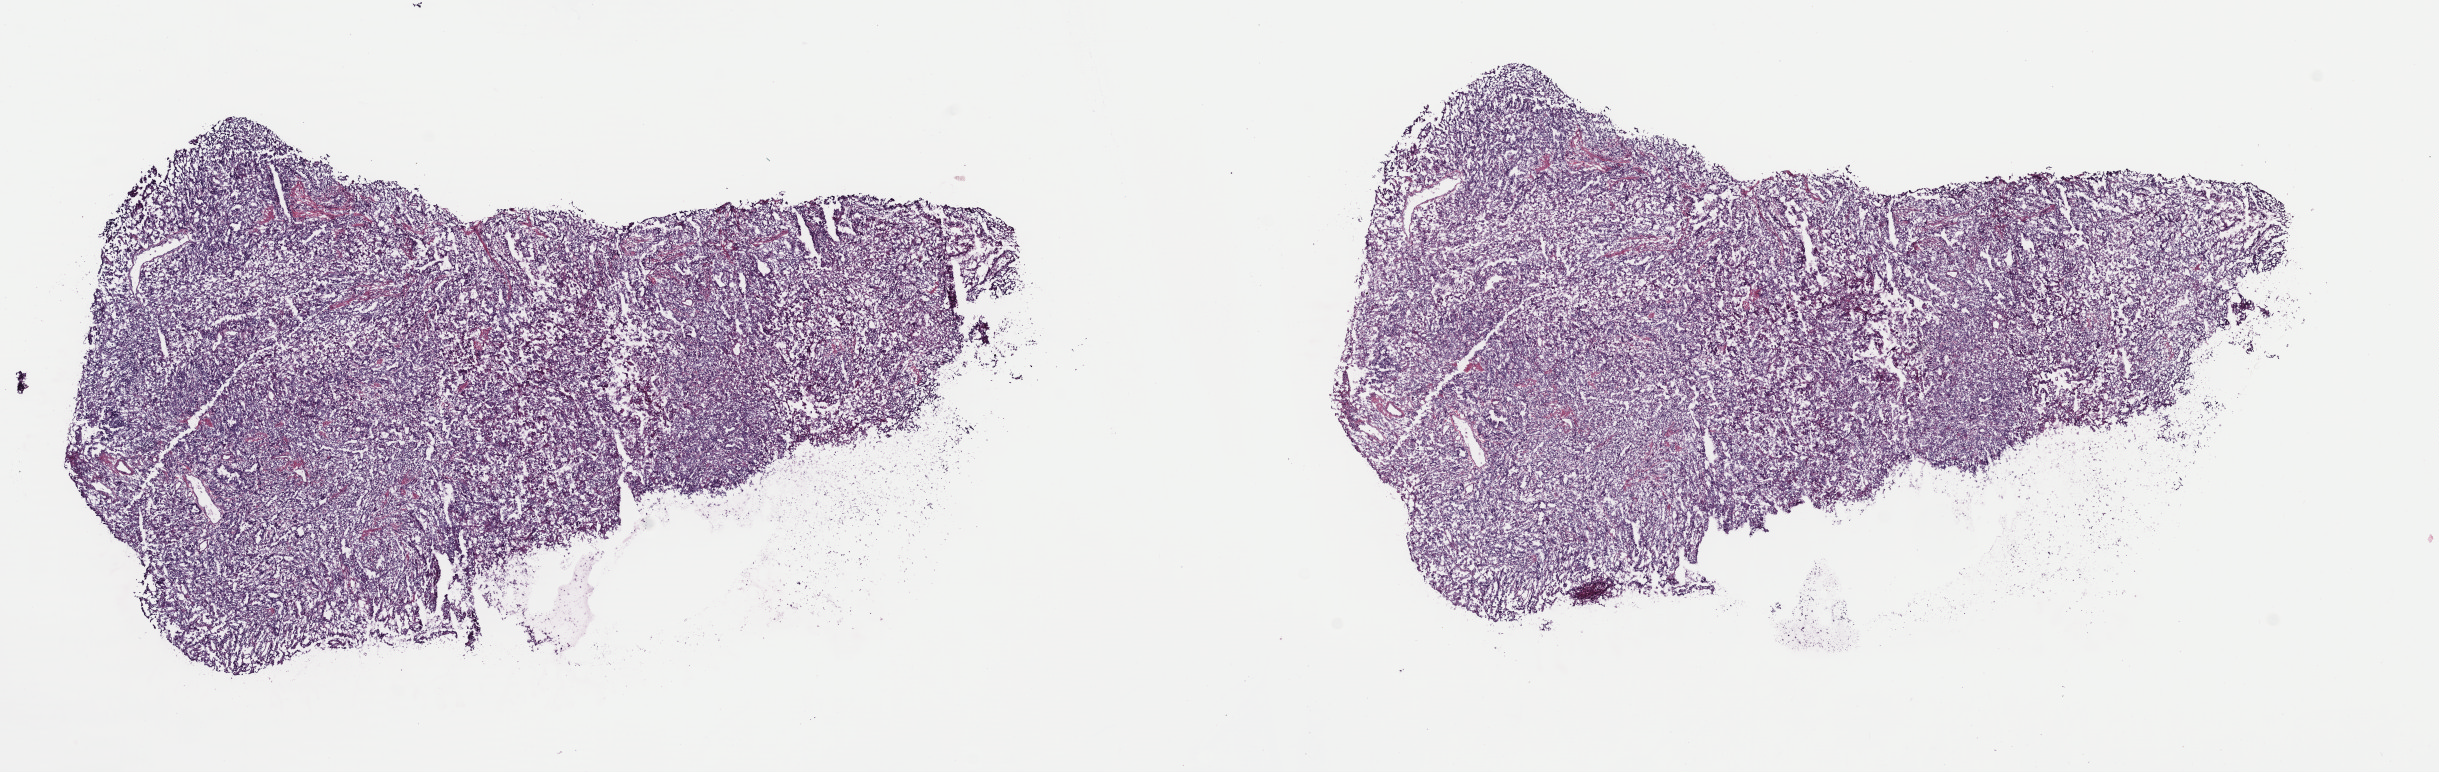
Digitized H&E tissue section (whole slide) — shown as a low-resolution overview of the whole scanned area (about 19.2 x 6.1 mm, from a 40x scan), frozen section from the top of the tissue portion, primary tumour sample from the stomach. Female, age 72 years at initial diagnosis. Histologic grade: G3 (poorly differentiated). Slide review estimates, as recorded: tumour cells 90%, tumour nuclei 90%, normal cells 0%, stromal cells 10%, necrosis 0%. Inflammatory infiltration, as recorded: lymphocyte infiltration 0%, monocyte infiltration 0%, neutrophil infiltration 0%.
AJCC pathologic stage: IIB (7th edition). TNM: T4a N0 M0. Pathologic diagnosis: Adenocarcinoma, NOS (fundus of stomach).